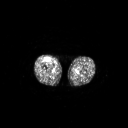
FDG PET of an extremity soft-tissue mass (from a PET/CT study), one axial slice; slice 242 of 311 in the series (ordered by position); 3.27 mm slice thickness; 128 × 128 image matrix, field of view 700 × 700 mm. Male patient, age 56 years. Case-level facts recorded for this patient, not image findings: histological type: pleiomorphic leiomyosarcoma; grade: intermediate; site of the primary tumour: right thigh.
Structures marked on this image (expert contour drawn on MRI and transferred to this co-registered scan by the dataset authors):
- gross tumour volume including surrounding oedema: bounding box (x1, y1, x2, y2) in pixels: (45, 57, 51, 62)